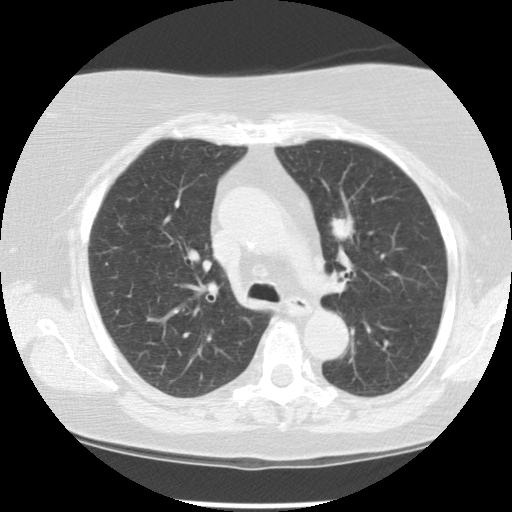
Chest CT (low-dose screening protocol), one axial image, first (baseline) screen, lung window (W 1500 / L -600 HU), standard (soft-tissue) reconstruction kernel (STANDARD), 120 kVp, 512 × 512 image matrix. Female, age 67 years at enrolment. Former smoker at enrolment.
• Expert-annotated lung lesion, box from (x=310, y=205) to (x=364, y=255) px.
• The exam's reader record, not a measurement of the box and not confirmed to be the same lesion: non-calcified nodule or mass ≥4 mm, left upper lobe, 13 × 10 mm, poorly defined margins, soft tissue attenuation.
• Lung cancer was diagnosed 399 days after this screen (after the second annual screen): adenocarcinoma, NOS, left upper lobe, moderately differentiated (G2), stage IIA (AJCC 6th edition), 23 mm at pathology.